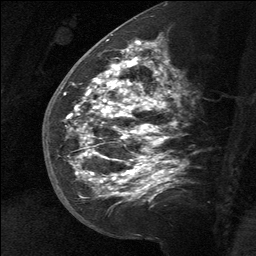
Breast MRI (dynamic contrast-enhanced), one sagittal slice. Position 34 of 64 along the scan axis. Dynamic contrast-enhanced study with each time point stored as its own series, time point 2 of 3 at this slice position (early post-contrast, ordered by acquisition time). 1.5 T. TE 4.8 ms, TR 27 ms. 2 mm slice thickness. 256 × 256 image matrix, field of view 180 × 180 mm. Patient: female, 39 years. From the clinical record (not read from this slice): setting: breast cancer imaged before/during neoadjuvant chemotherapy; receptor status: HER2-positive.
Annotated regions visible in this slice (semi-automatic segmentation, software-assisted and operator-edited):
- analysis volume of interest (the breast-tissue region the enhancement analysis was run in; not a lesion): bounding box <58,40,172,217> (left, top, right, bottom; pixels)
- tumour enhancement mask (voxels above the 90 % enhancement threshold inside the analysis volume of interest): <66,41,161,197>